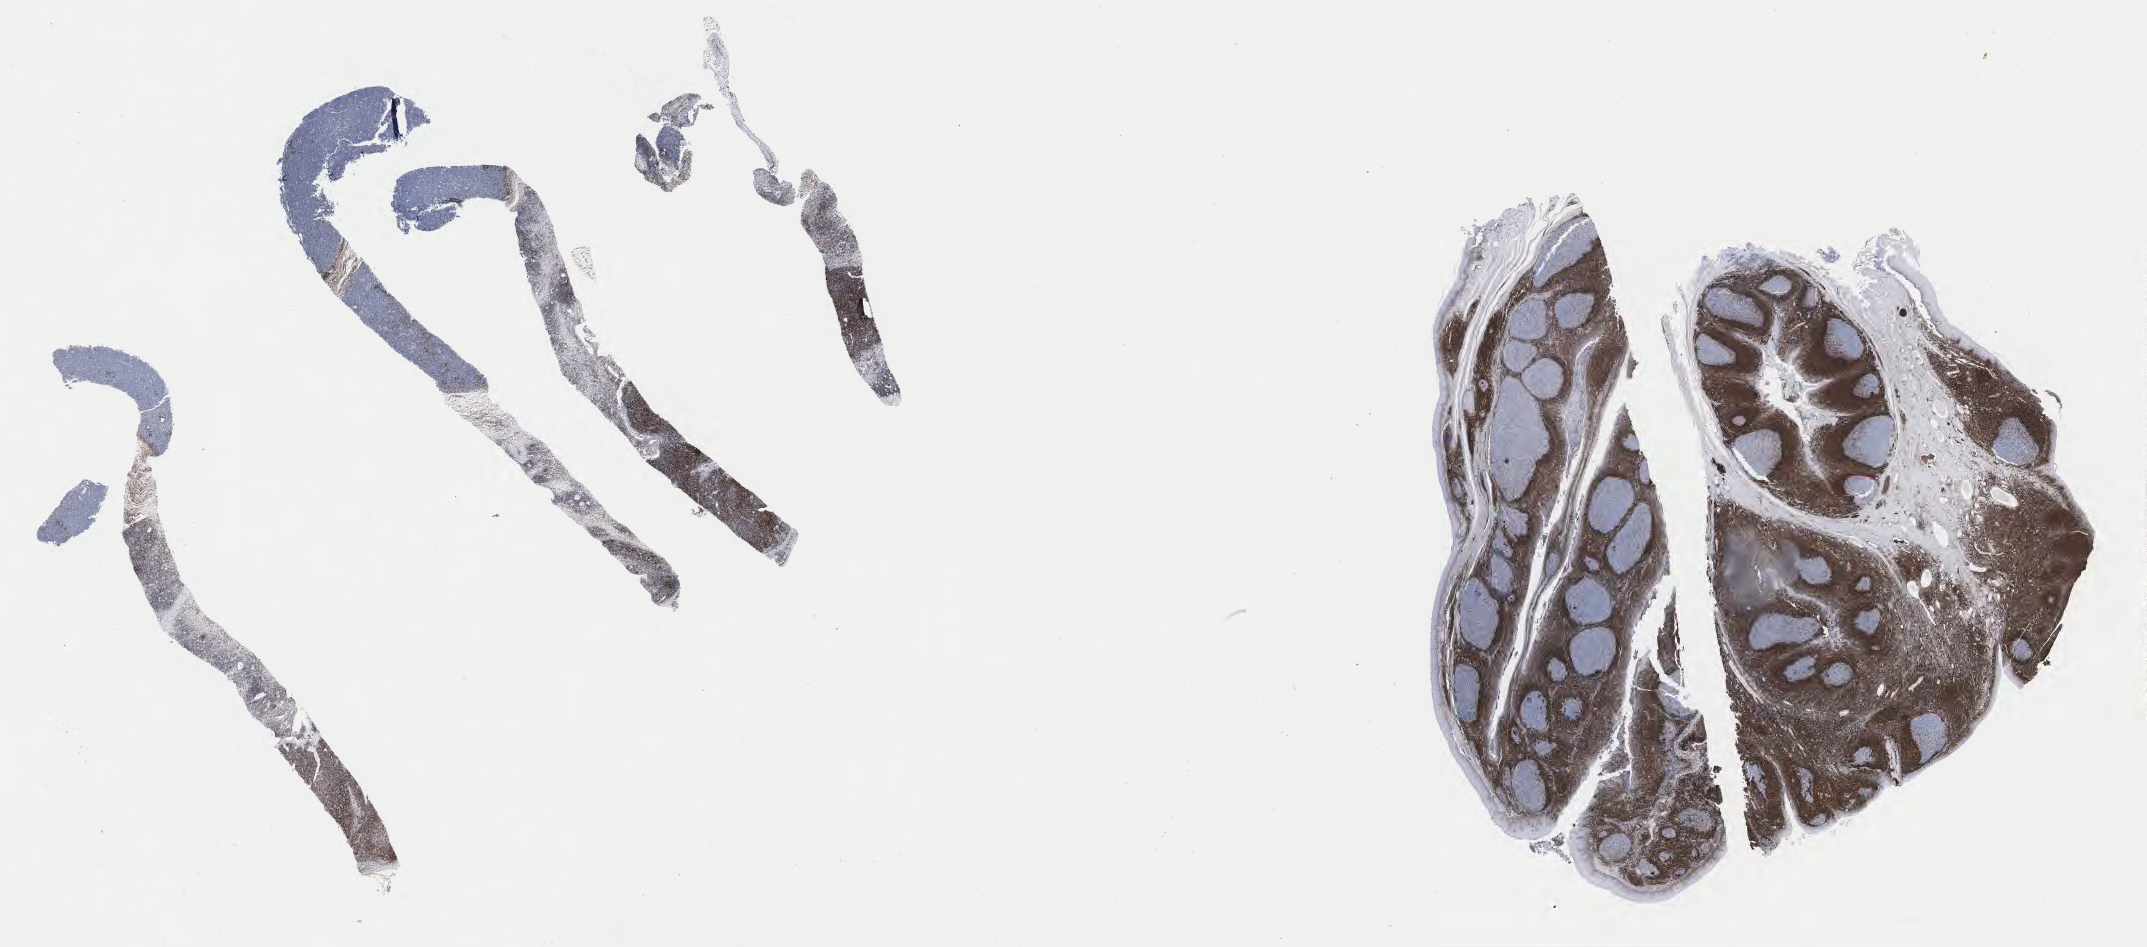
Whole-slide image, immunohistochemical stain for BCL2, low-resolution overview of the scanned area, about 34.7 x 15.3 mm, tumor tissue. Patient male; age 47 years.
Histologic diagnosis: Burkitt lymphoma, NOS.